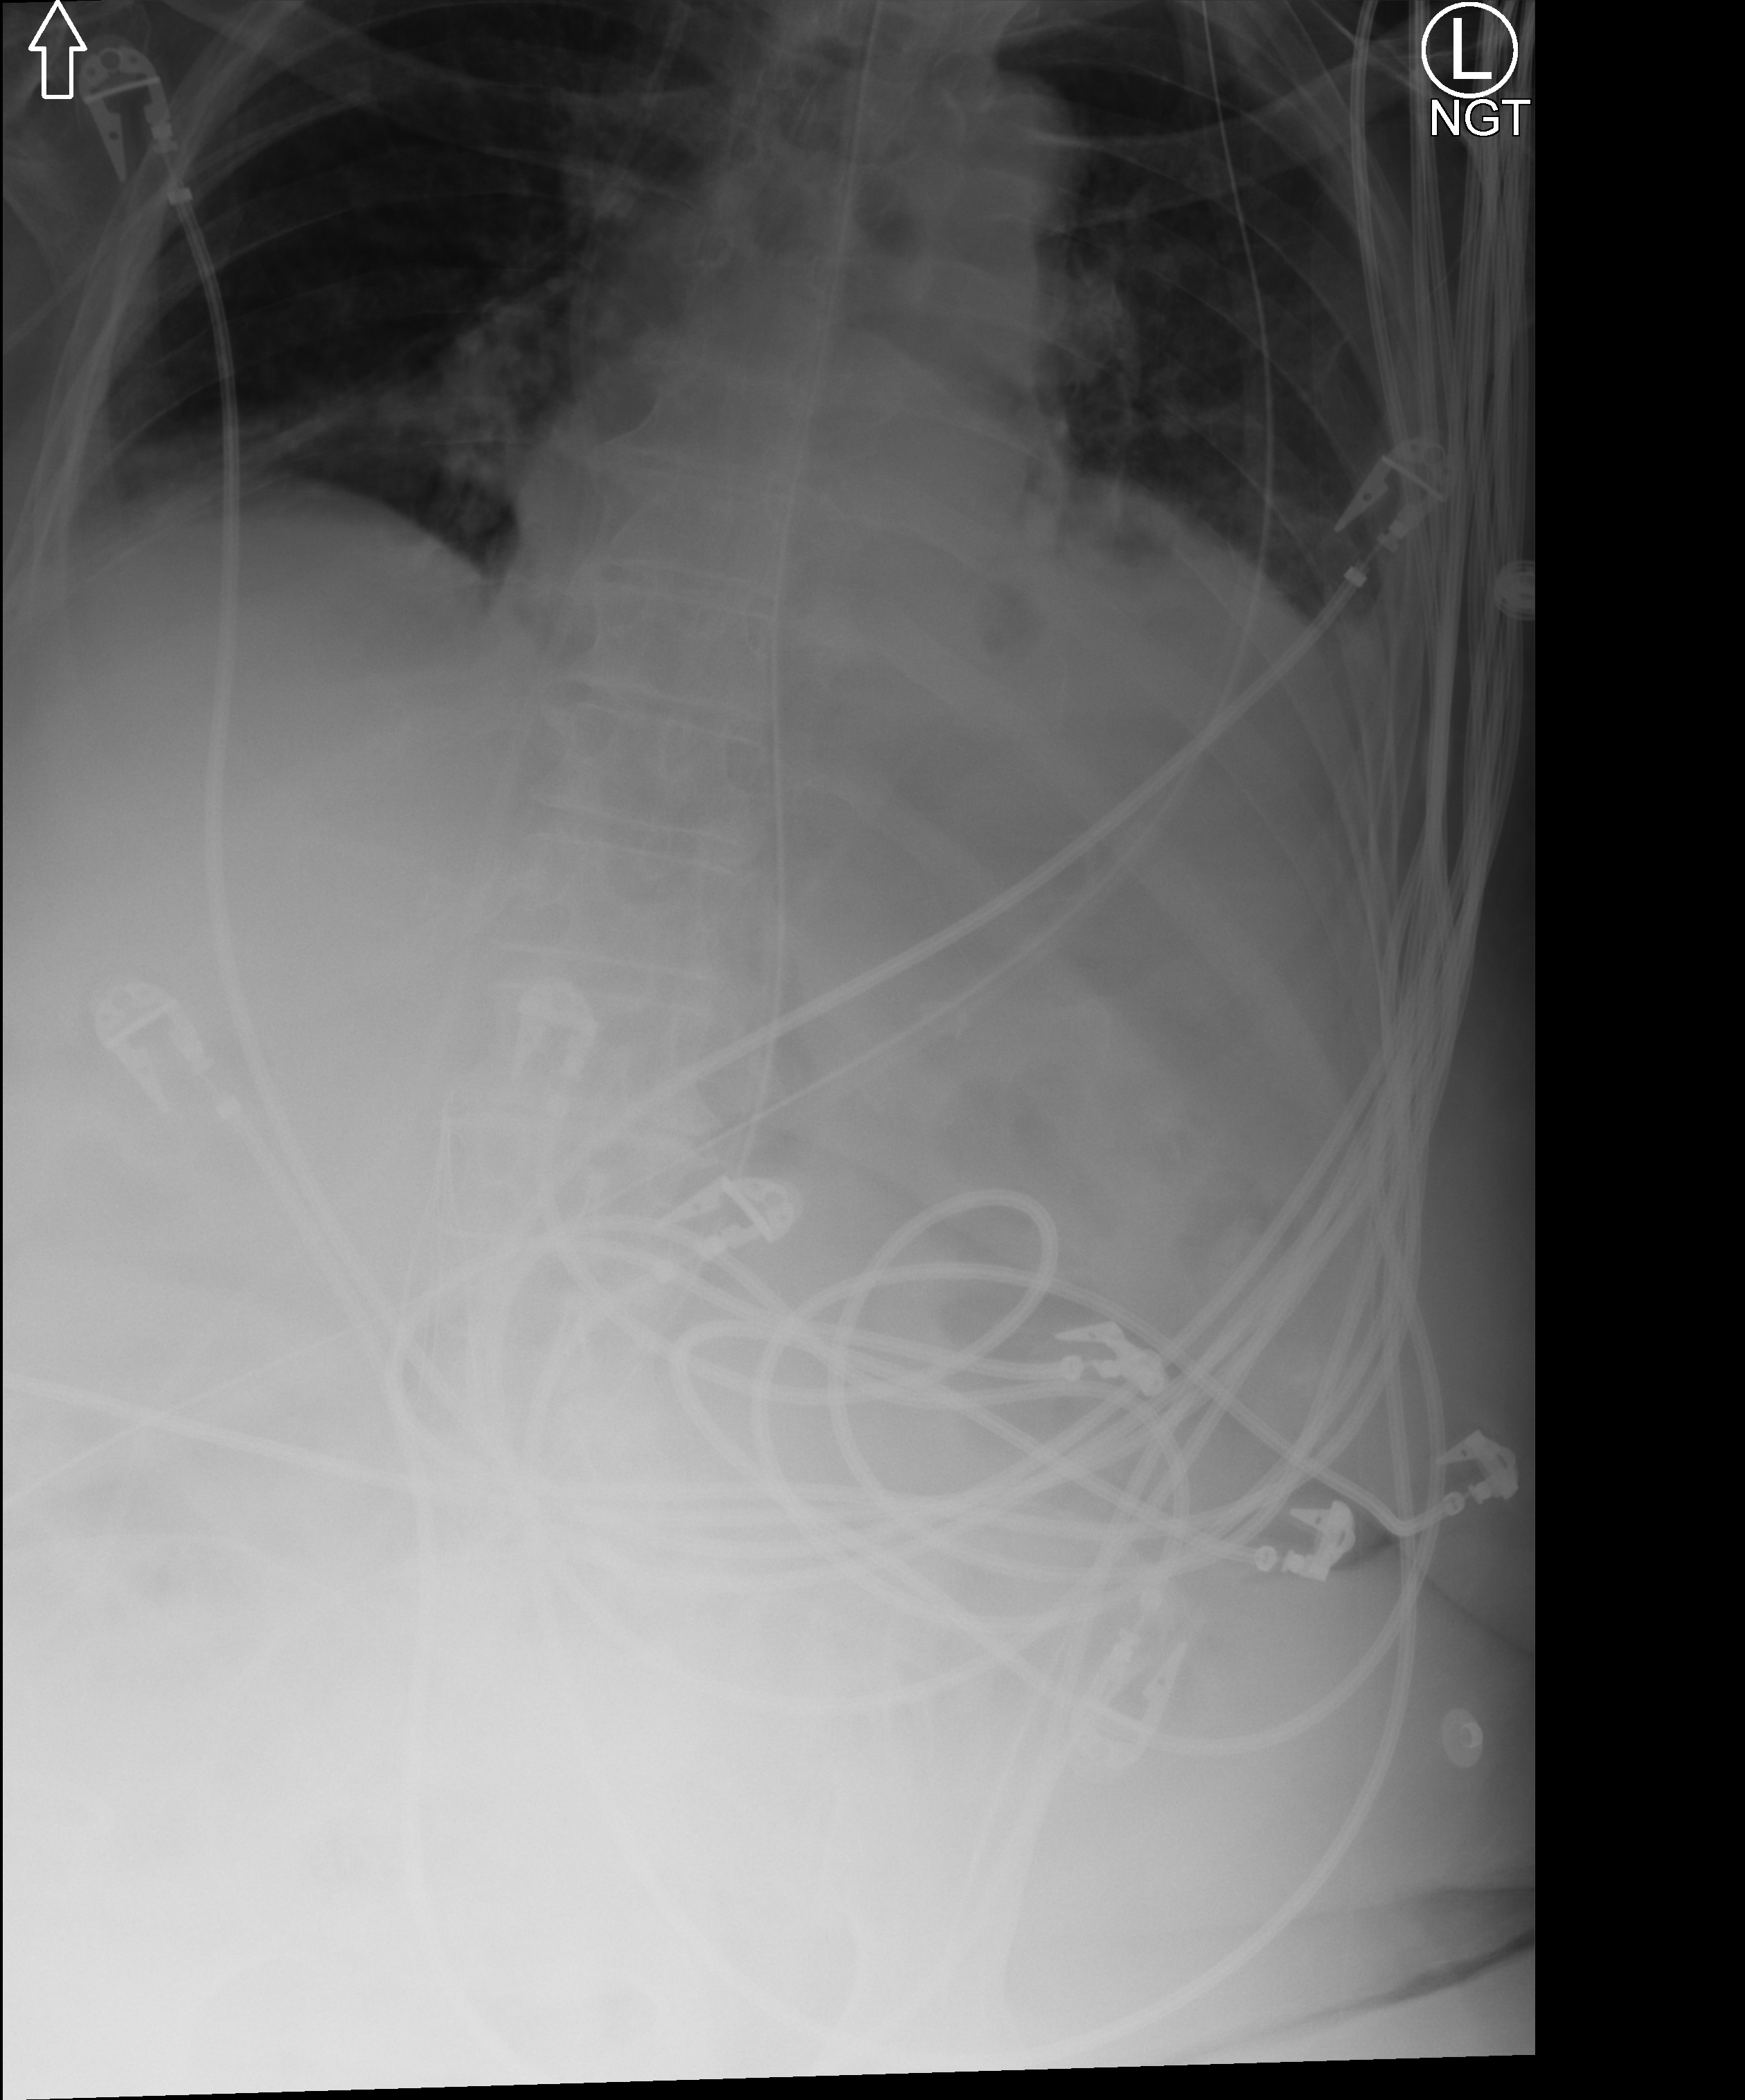
Bedside abdomen radiograph (computed radiography); anteroposterior (AP) projection. Female patient hospitalised with COVID-19, age 75–90 years.
From the hospital-stay record, not from the radiograph (when in the stay this image was taken is not recorded):
- chronic kidney disease (admission record): no
- admitted to intensive care during this hospital stay: yes